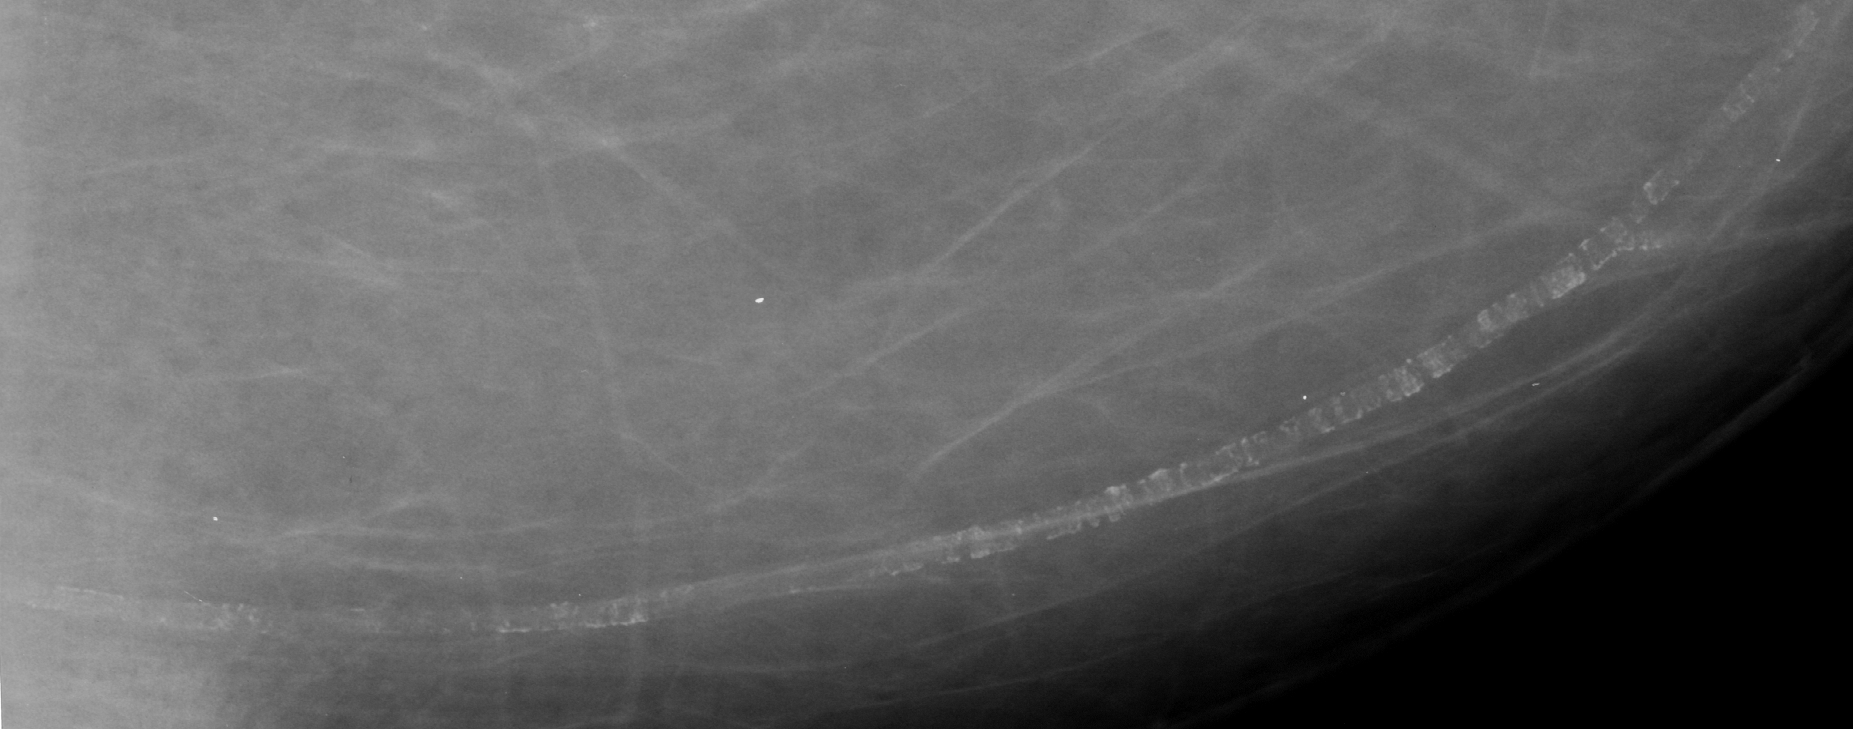
Region of interest cut from a scanned film mammogram (one marked finding), left breast, CC view, BI-RADS breast density category 2 (scale 1–4).
Marked abnormality: calcifications, morphology vascular / coarse / lucent centered; BI-RADS assessment category 2; benign without callback (not worked up further).